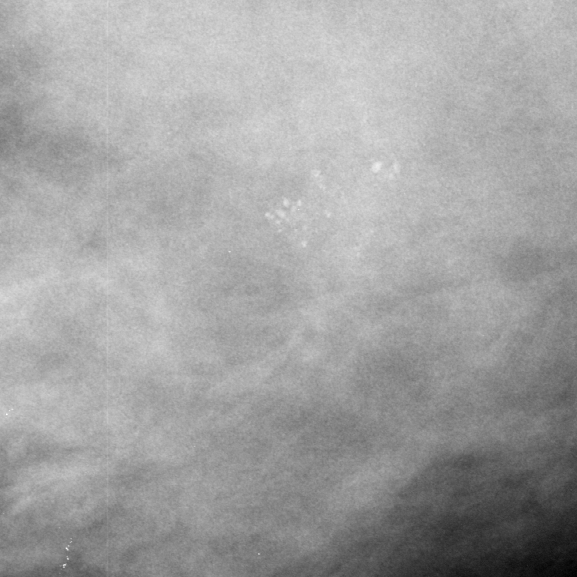
Region of interest cut from a scanned film mammogram (one marked finding), left breast, CC view, BI-RADS breast density category 4 (scale 1–4).
Calcifications, morphology pleomorphic, distribution clustered; BI-RADS assessment category 4; subtlety rating 4 on a 1 (subtle) to 5 (obvious) scale; pathology (as recorded): benign.